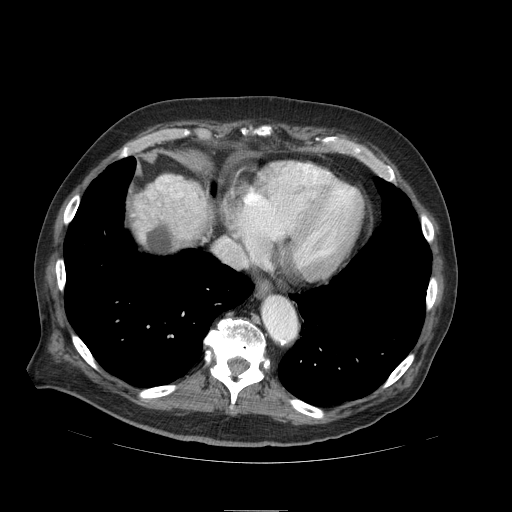
Contrast-enhanced abdominal CT (liver protocol), one axial slice; reconstruction kernel STANDARD; 120 kVp; soft-tissue window (W 400 / L 40 HU); 2.5 mm slice thickness; 512 × 512 image matrix, field of view 440 × 440 mm. From the clinical record (not read from this slice): diagnosis: hepatocellular carcinoma (patient treated with transarterial chemoembolisation; whether this scan precedes or follows treatment is not stated here); TNM stage (as recorded): Stage-IIIA; Child-Pugh class: B; tumour differentiation: well differentiated; tumour nodularity: multinodular.
Outlined on this slice (semi-automatically segmented with operator editing):
- abdominal aorta: bounding box [x1, y1, x2, y2] px = [263, 297, 296, 341]
- liver parenchyma outside the tumour (the mass and vessels are separate outlines, so this box may not span the whole liver): [130, 174, 182, 248]
- mass: [129, 173, 215, 248]